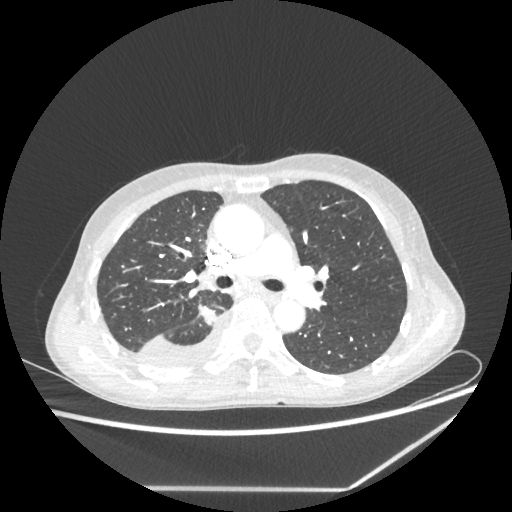
Chest CT, one axial slice; slice 144 of 237 in the series (ordered by position); lung window (W 1500 / L -600 HU); 1.25 mm slice thickness; 512 × 512 image matrix, field of view 364 × 364 mm. Female patient, age 59 years. From the clinical record (not read from this slice): clinical TNM (as recorded): T1c N1 M1.
Outlined on this slice (bounding box drawn by a radiologist):
- lung tumour (recorded histology: adenocarcinoma): bounding box <197,303,218,327> (left, top, right, bottom; pixels)